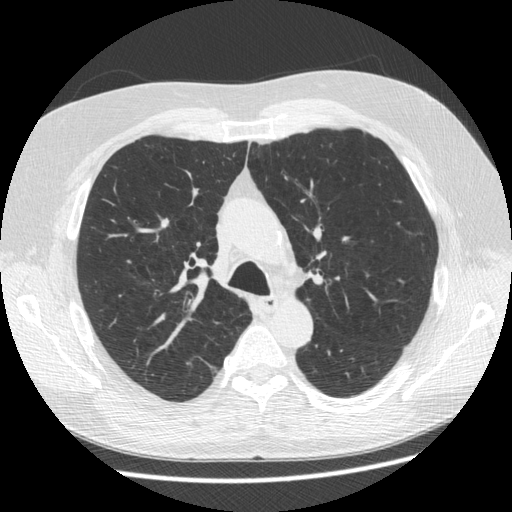
Chest CT (low-dose screening protocol), one axial image, third screening round (two years after baseline), lung window (W 1500 / L -600 HU). Male, age 63 years at enrolment.
Lesion marked by an expert reader, box from (x=150, y=209) to (x=182, y=238) px. The screening reader recorded 2 non-calcified nodules or masses ≥4 mm on this exam (right upper lobe, left upper lobe); which of them this box marks is not recorded. Official screen result: positive, other. Participant outcome: lung cancer diagnosed 342 days after this screen — adenocarcinoma, NOS, right upper lobe, stage IIA (AJCC 6th edition), 8 mm at pathology.